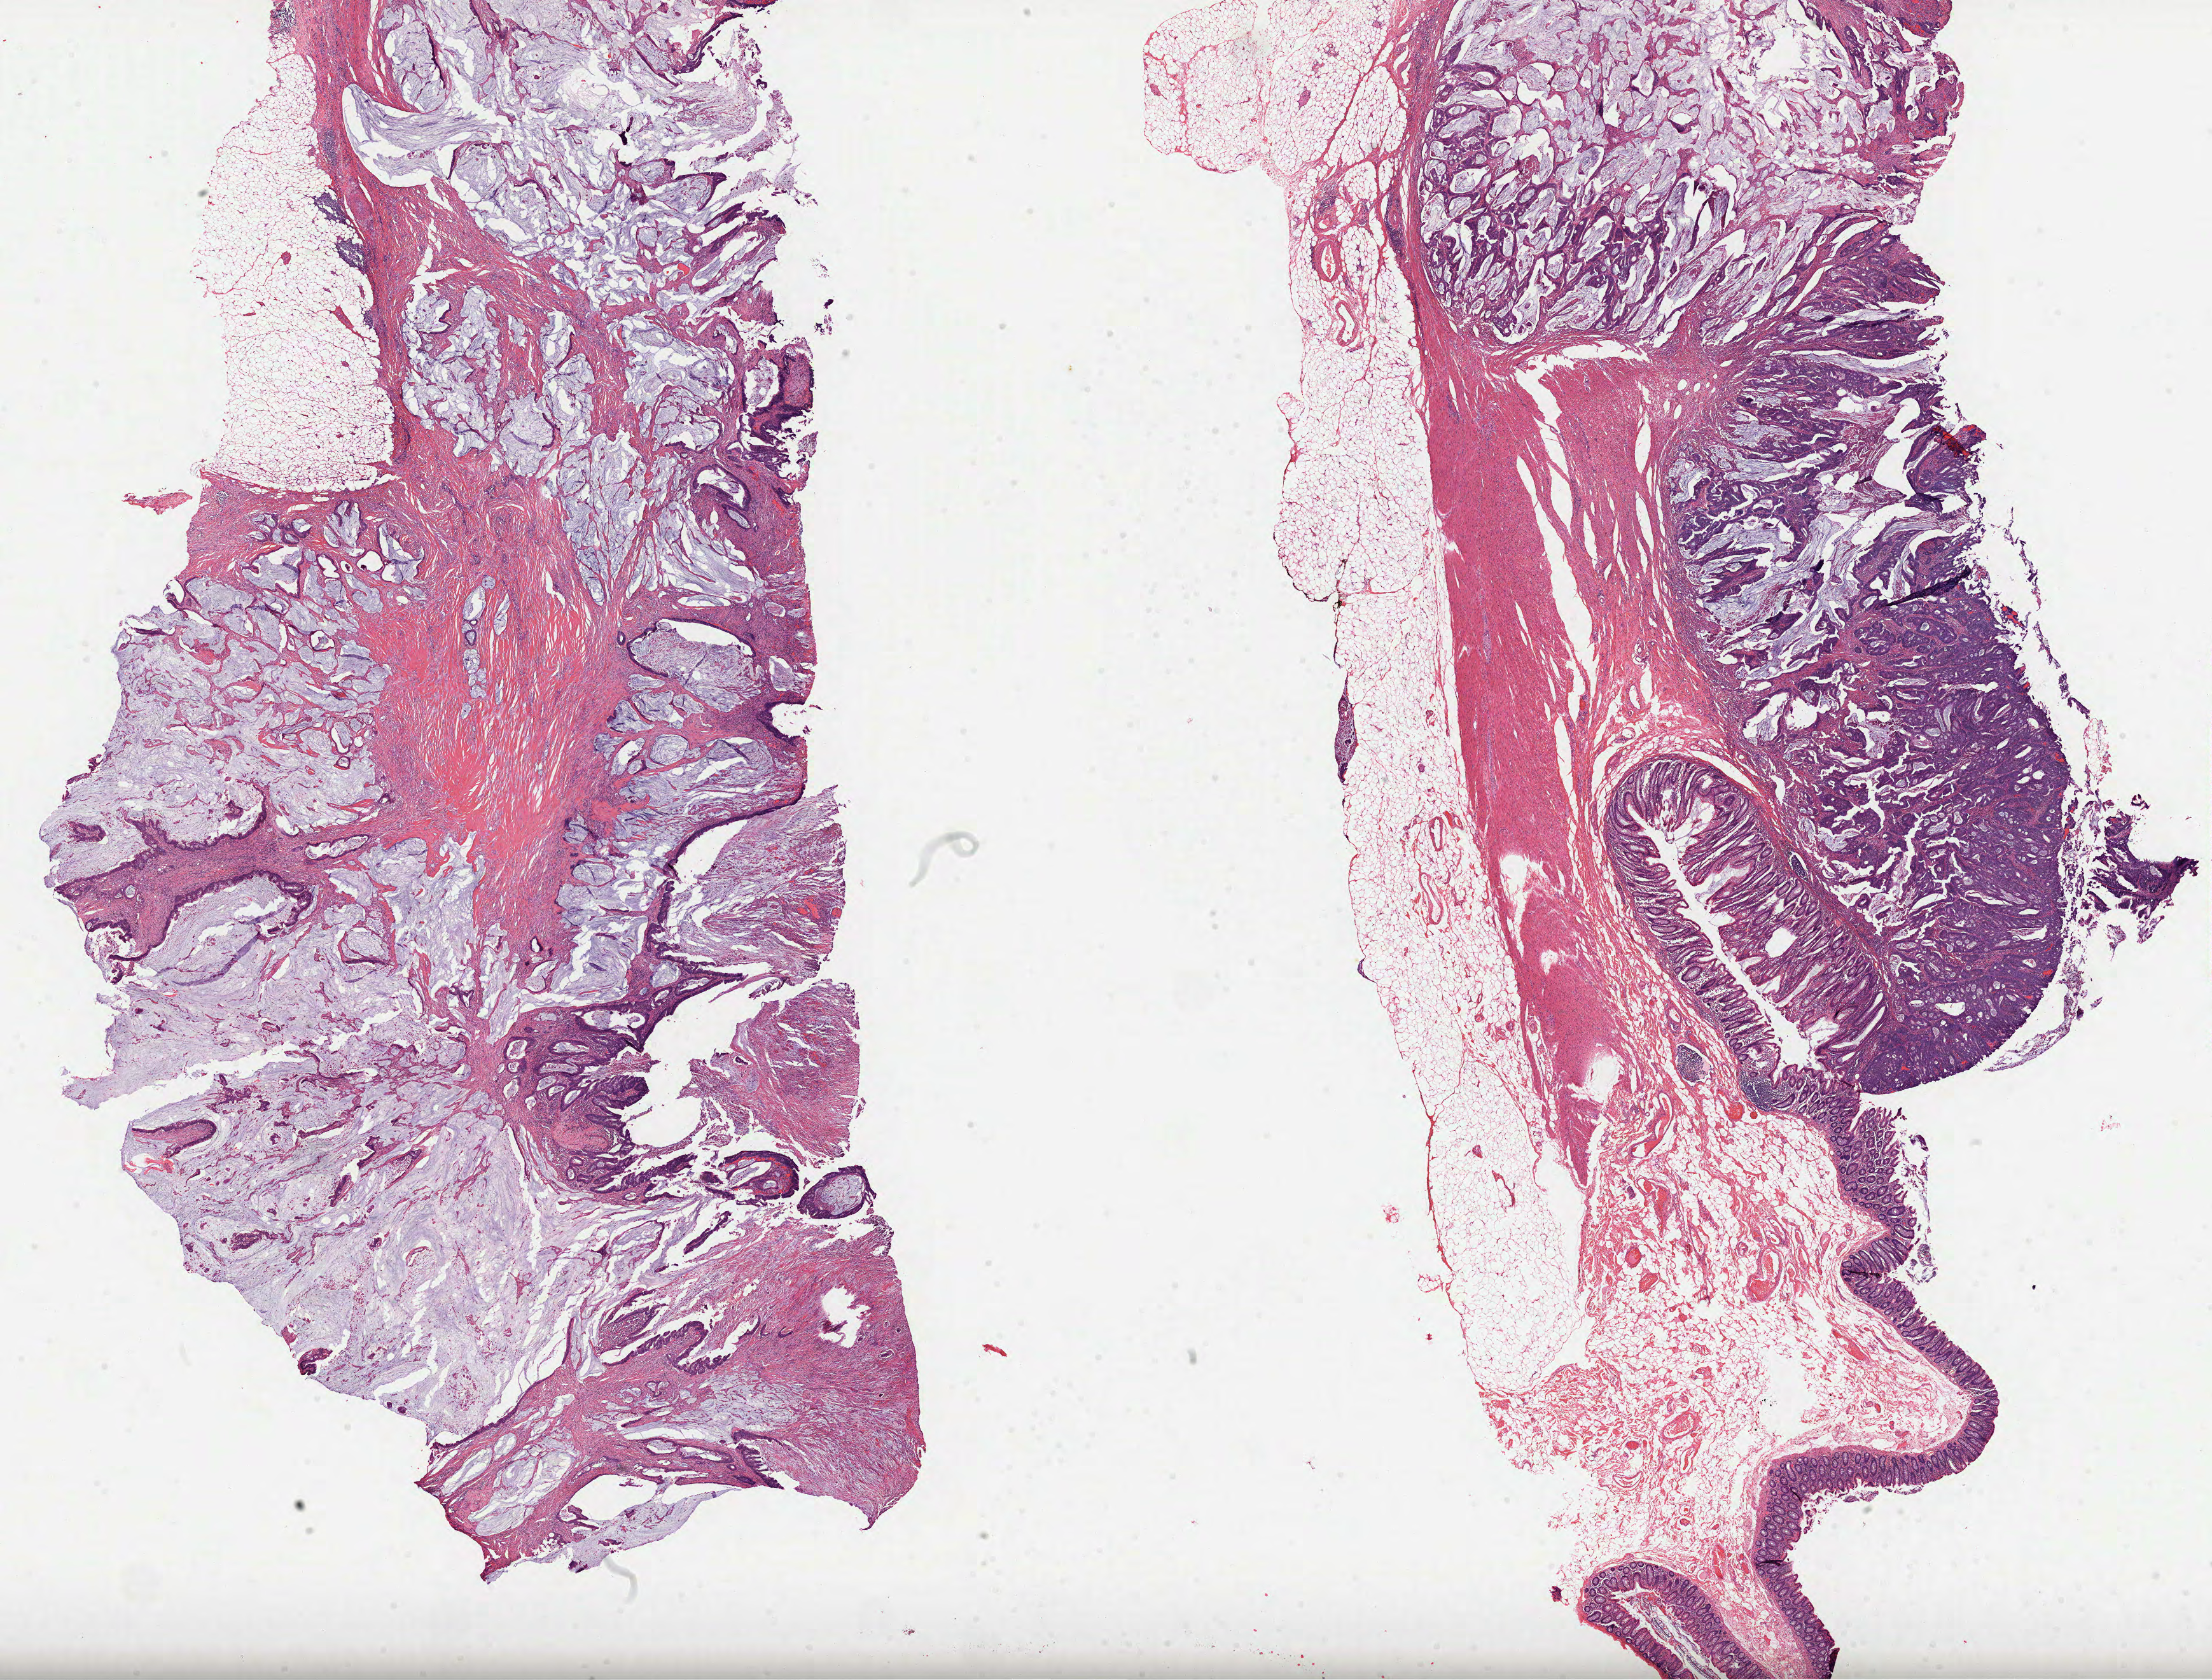
Digitized Hematoxylin and eosin (H&E) stained tissue section (whole slide) — shown as a low-resolution overview of the whole scanned area (about 28.0 x 21.3 mm, slide scanned at 40x); FFPE section; colon, primary tumour sample. Patient: female, age at initial diagnosis 68 years.
- histologic diagnosis: Mucinous adenocarcinoma (cecum)
- lymph nodes positive (case pathology): 1 of 18 examined
- AJCC pathologic stage: IIIB (6th edition)